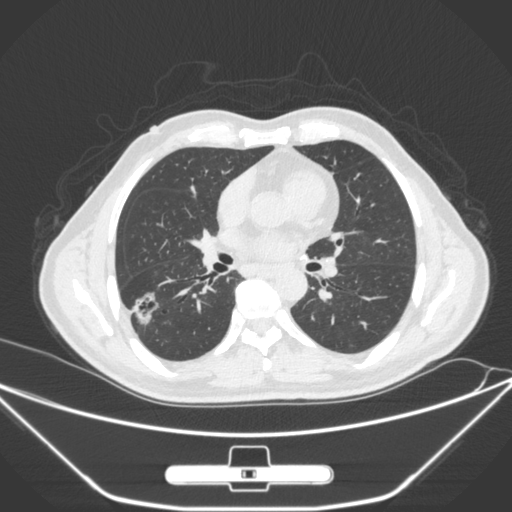
Chest CT, one axial slice. Slice 148 of 310 in the series (ordered by position). 120 kVp. Lung window (W 1500 / L -600 HU). 1 mm slice thickness. 512 × 512 image matrix, field of view 398 × 398 mm. Patient: male, 71 years. Case-level facts recorded for this patient, not image findings: clinical TNM (as recorded): T1c N0 M0; histopathological grade: G2.
Structures marked on this image (bounding box drawn by a radiologist):
- lung tumour (recorded histology: adenocarcinoma): bounding box <127,290,166,330> (left, top, right, bottom; pixels)